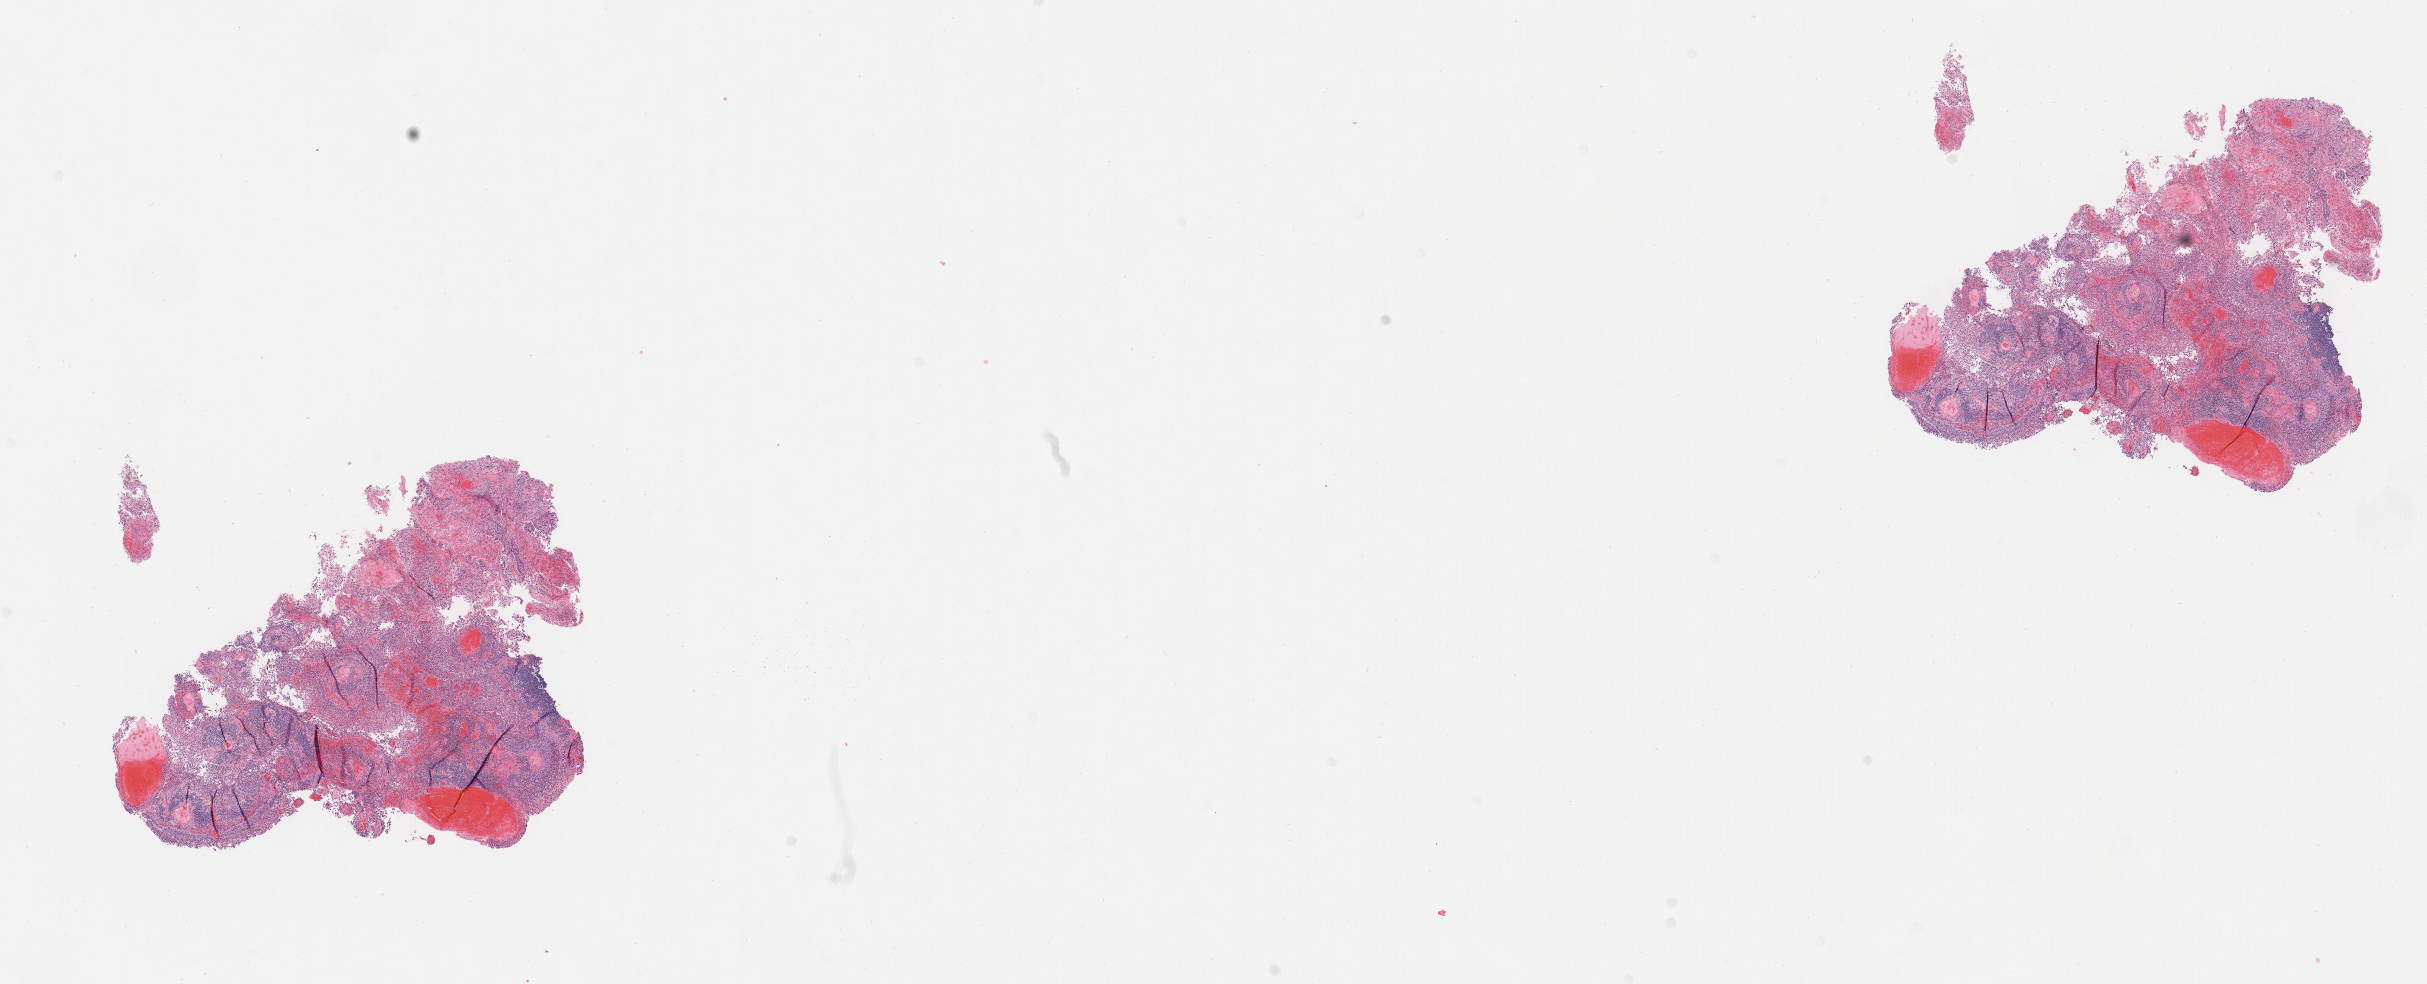
Whole-slide image, hematoxylin and eosin (H&E) stain, whole scanned area (about 19.6 x 8.0 mm) shown as a low-resolution overview; specimen: tumor tissue; site: cervix. Female patient, age 52 years.
Histologic diagnosis: Squamous cell carcinoma, large cell, nonkeratinizing, NOS.